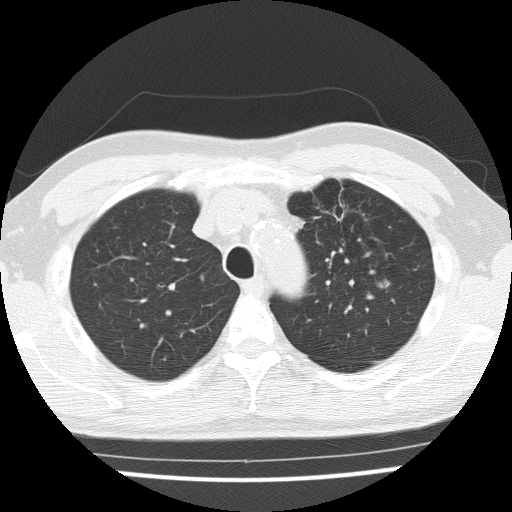
Low-dose screening chest CT, one axial slice; position 115 of 154 along the scan axis; reconstruction kernel FC51; lung window (W 1500 / L -600 HU); 512 × 512 image matrix, field of view 330 × 330 mm.
Annotated regions visible in this slice (manually delineated by an expert):
- lesion 1 (tumor, upper lobe of left lung): box from (x=380, y=283) to (x=389, y=287) px